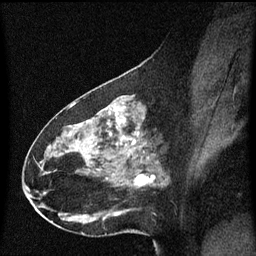
Breast MRI (dynamic contrast-enhanced), one sagittal slice. Slice 30 of 60 in the series (ordered by position). Dynamic contrast-enhanced series, image 2 of 3 at this slice position (ordered by acquisition). 1.5 T. TE 4.2 ms, TR 8.4 ms. 2 mm slice thickness. 256 × 256 image matrix. Patient: female, 49 years. Case-level facts recorded for this patient, not image findings: setting: breast cancer imaged before/during neoadjuvant chemotherapy; receptor status: HR-positive, HER2-negative.
Annotated regions visible in this slice (semi-automatically segmented with operator editing):
- analysis volume of interest (the breast-tissue region the enhancement analysis was run in; not a lesion): bounding box <27,96,170,221> (left, top, right, bottom; pixels)
- tumour enhancement mask (voxels above the 70 % enhancement threshold inside the analysis volume of interest): <108,114,140,181>